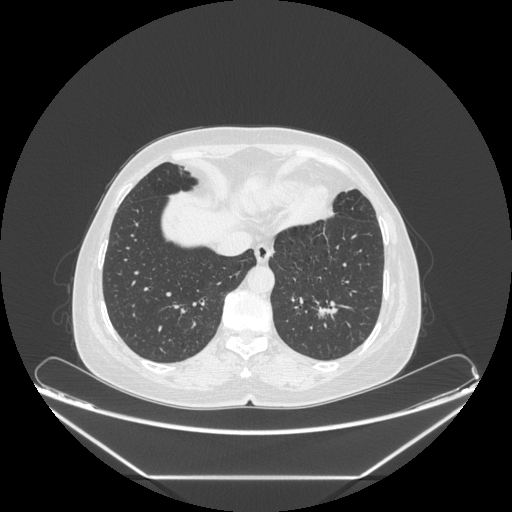
Chest CT, one axial slice. Position 66 of 241 along the scan axis. 120 kVp. Lung window (W 1500 / L -600 HU). 1.25 mm slice thickness. 512 × 512 image matrix, field of view 451 × 451 mm. Patient: female, 63 years. From the clinical record (not read from this slice): clinical TNM (as recorded): T1c N0 M0; histopathological grade: G2-3.
Annotated regions visible in this slice (bounding box drawn by a radiologist):
- lung tumour (recorded histology: adenocarcinoma): box from (x=313, y=297) to (x=347, y=333) px